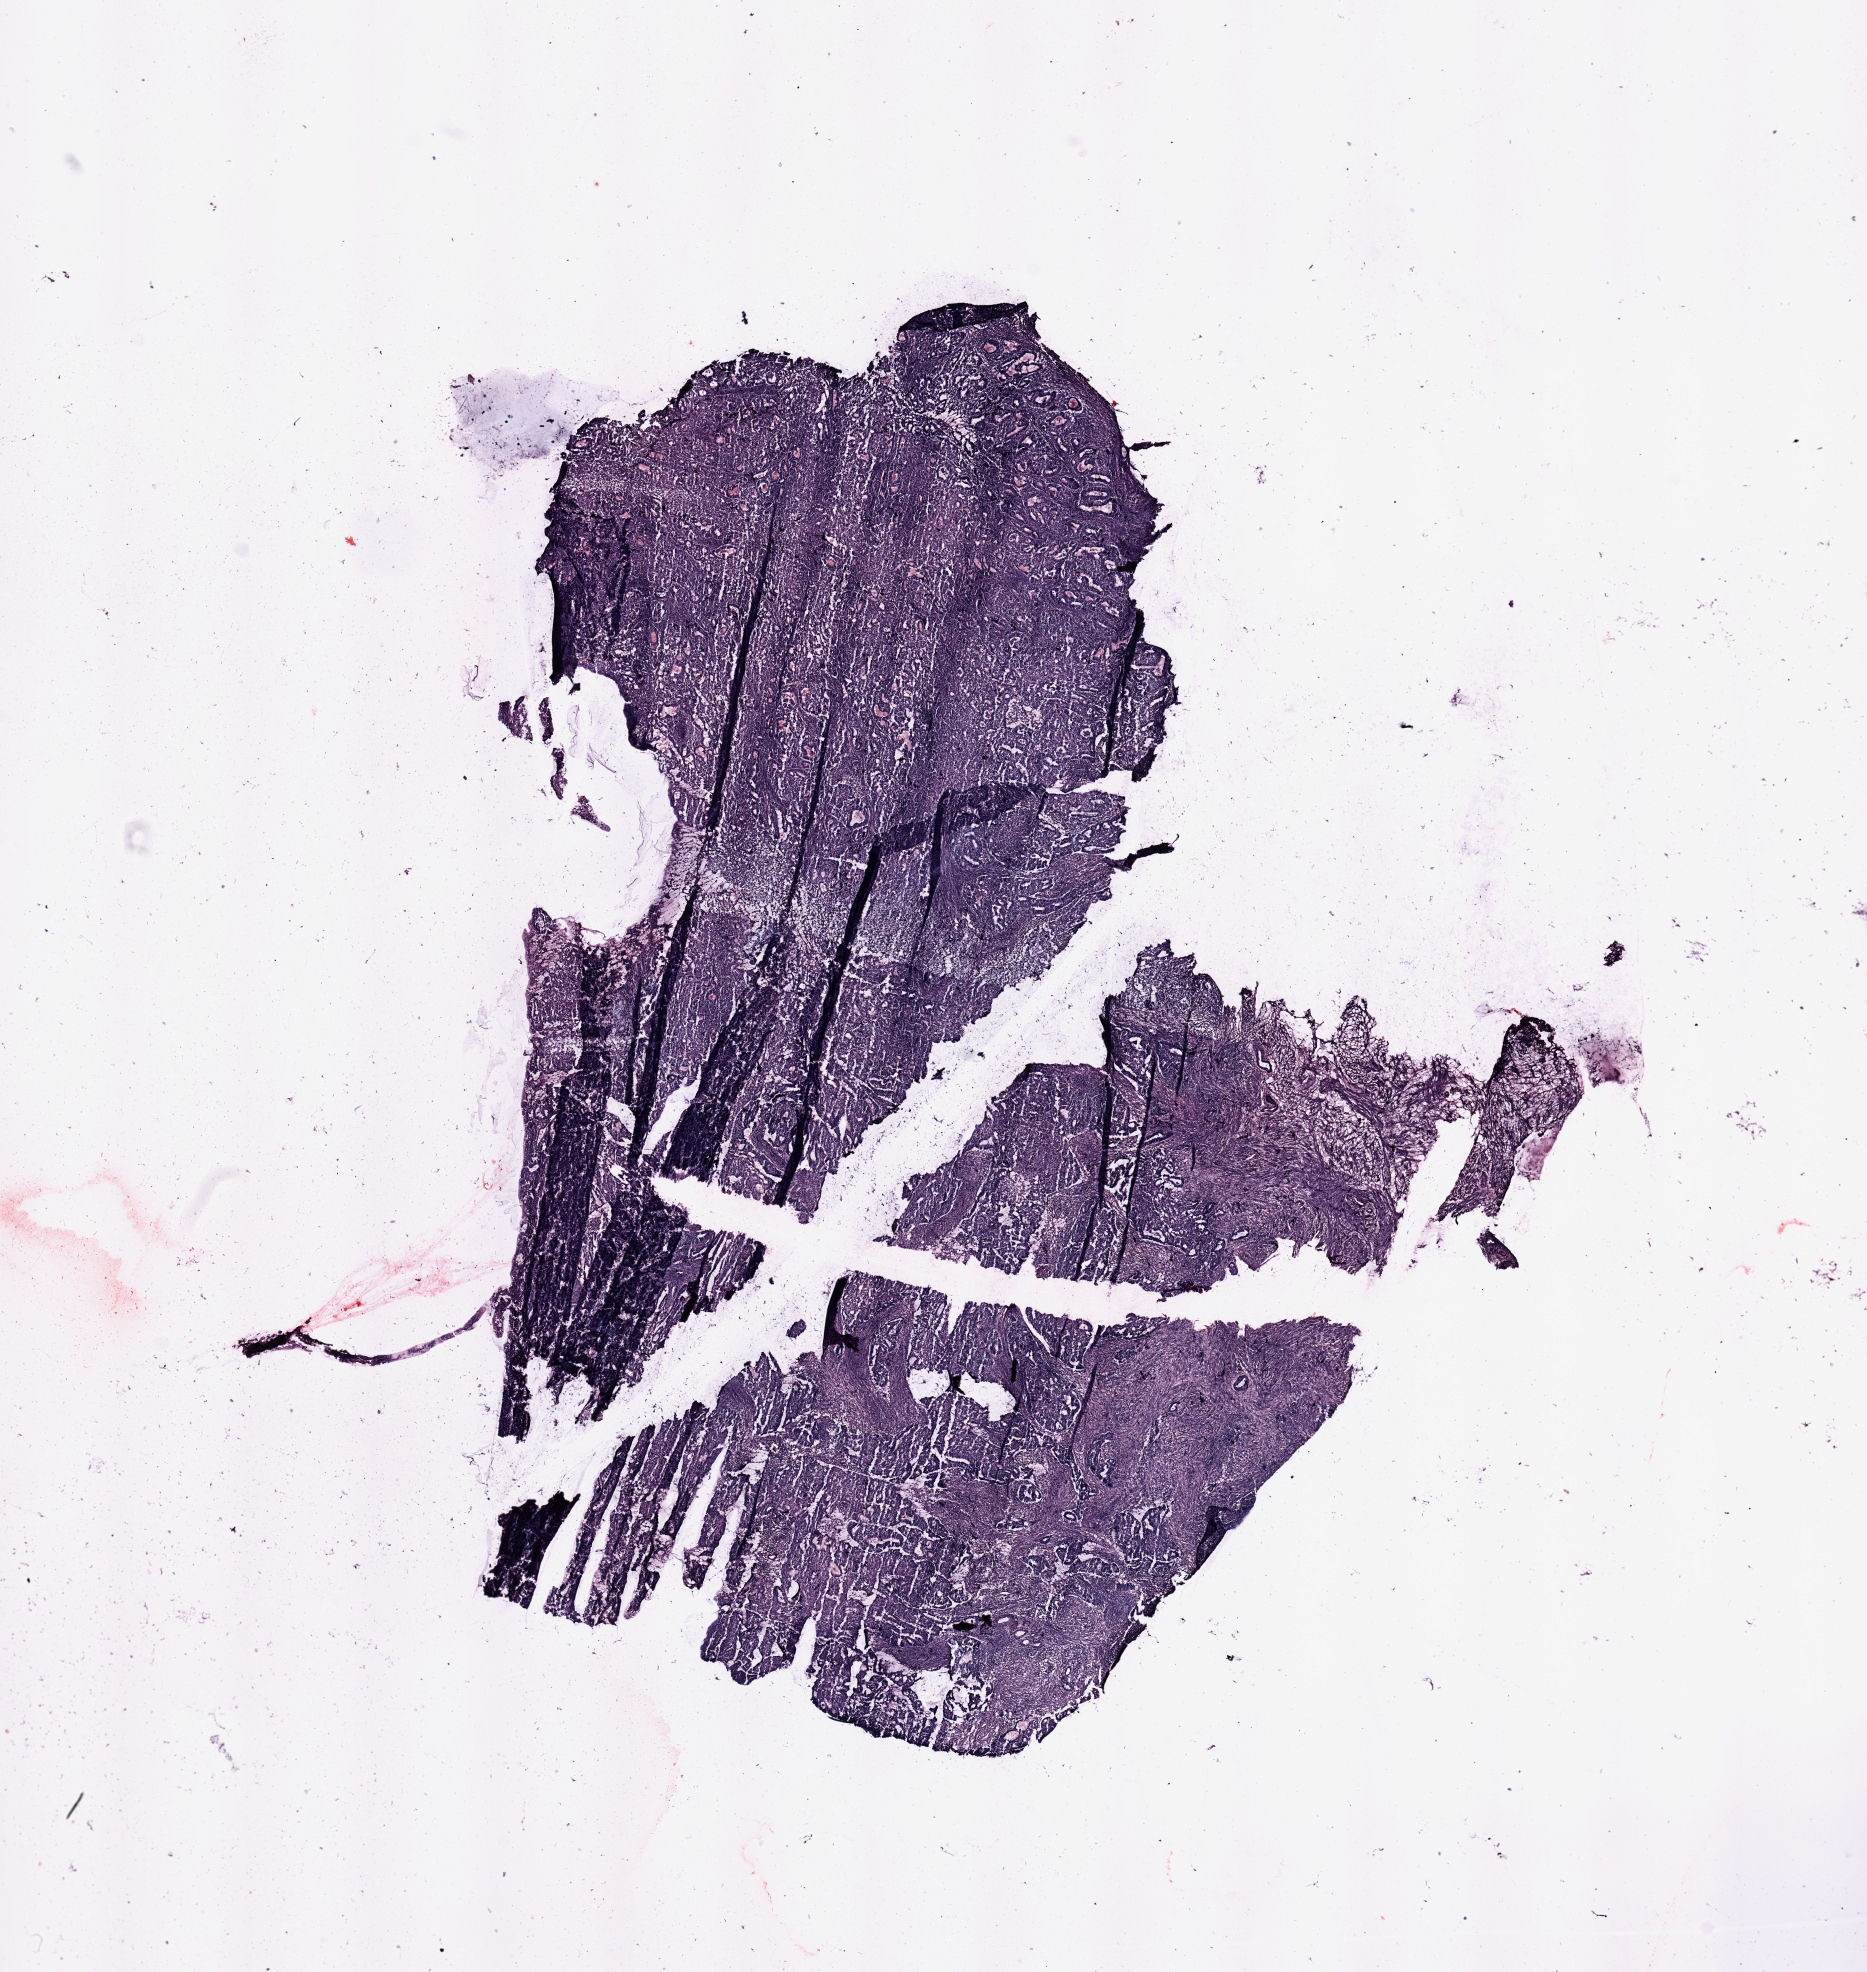
Digitized H&E-stained tissue section (whole slide) — whole scanned area (about 14.8 x 15.6 mm) shown as a low-resolution overview; tumour tissue sample, uterus. Female, 62 y/o. Histologic grade: G2 (moderately differentiated).
AJCC pathologic stage: I. Histologic diagnosis: Endometrioid adenocarcinoma, NOS.